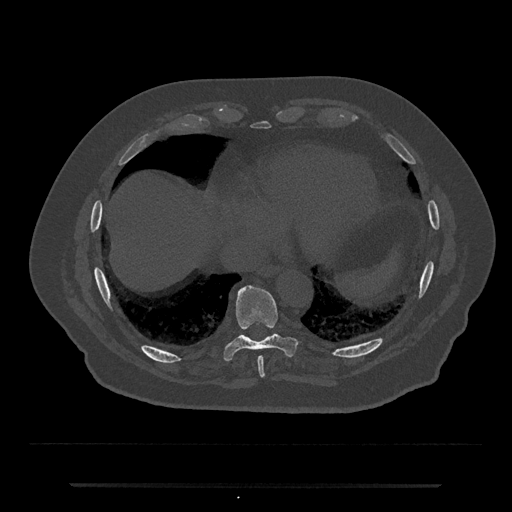
CT including the spine, one axial slice; position 760 of 797 along the scan axis; 120 kVp; bone window (W 1800 / L 400 HU); 0.5 mm slice thickness; 512 × 512 image matrix. Patient: male, 80 years. Case-level facts recorded for this patient, not image findings: primary cancer: prostate; vertebrae with lytic lesions (as recorded): L1, T11.
Annotated regions visible in this slice (semi-automatic segmentation, software-assisted and operator-edited):
- T8 vertebra: bounding box (x1, y1, x2, y2) in pixels: (257, 357, 265, 378)
- T9 vertebra: (223, 284, 296, 361)